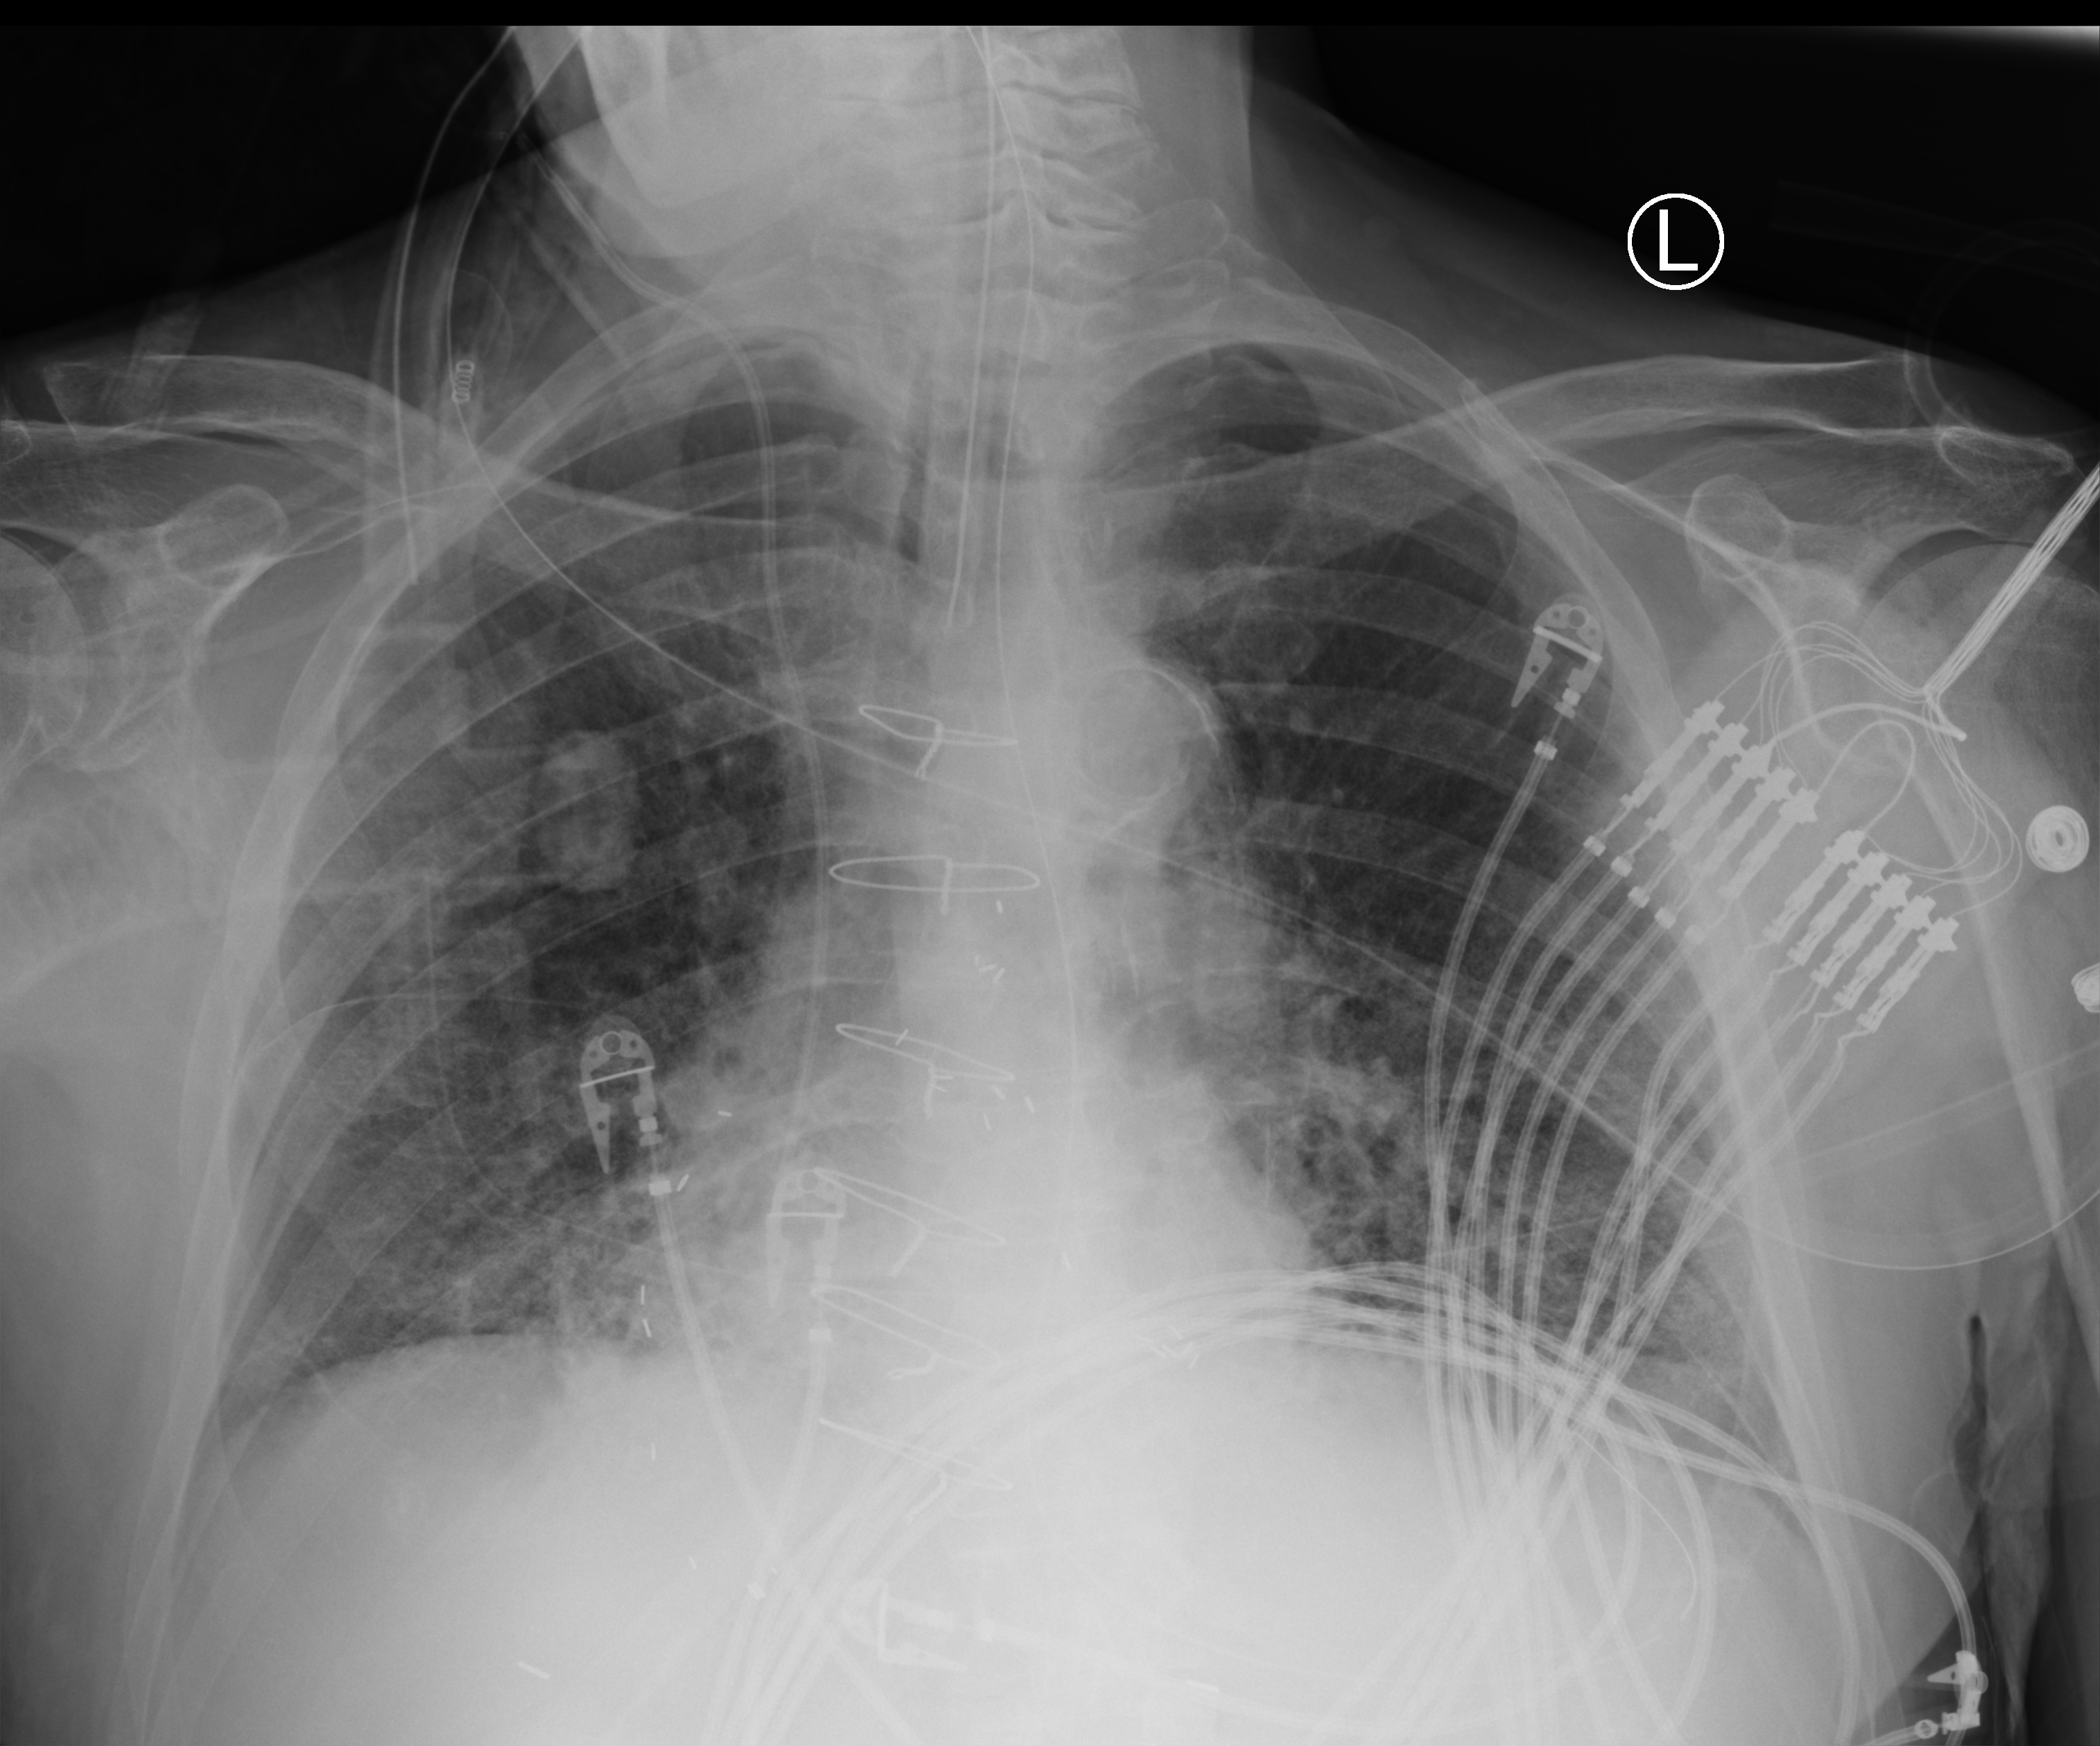
Bedside chest radiograph (computed radiography), anteroposterior (AP) projection. Patient hospitalised with COVID-19; male, aged 75–90 years.
Admission-level facts for this patient (not findings on this image; timing relative to this image not recorded): hypertension (admission record): yes.